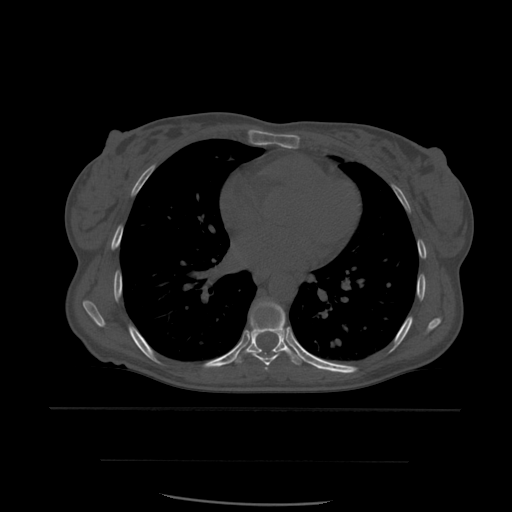
CT including the spine, one axial slice. Position 365 of 574 along the scan axis. Bone window (W 1800 / L 400 HU). 512 × 512 image matrix, field of view 392 × 392 mm. Patient age 48 years. From the clinical record (not read from this slice): primary cancer: lung.
Outlined on this slice (semi-automatically segmented with operator editing):
- T6 vertebra: bounding box [x1, y1, x2, y2] px = [266, 306, 285, 369]
- T7 vertebra: [252, 327, 286, 371]
- T8 vertebra: [232, 301, 303, 366]